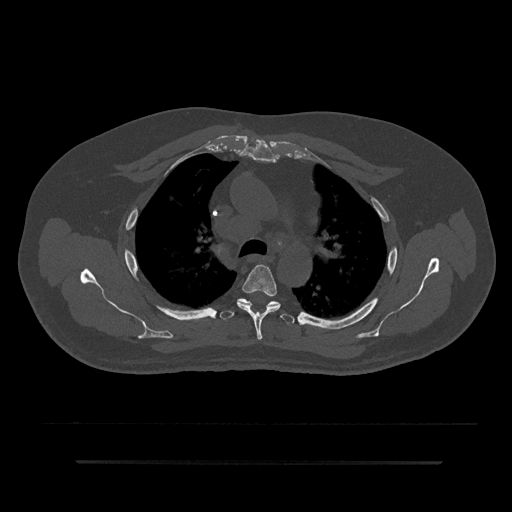
CT including the spine, one axial slice; position 606 of 797 along the scan axis; reconstruction kernel Br40s/3; 120 kVp; bone window (W 1800 / L 400 HU); 0.5 mm slice thickness; 512 × 512 image matrix, field of view 464 × 464 mm. Patient: male, 59 years. From the clinical record (not read from this slice): primary cancer: bile ducts; vertebrae with lytic lesions (as recorded): T10.
Outlined on this slice (semi-automatically segmented with operator editing):
- T4 vertebra: box from (x=237, y=265) to (x=281, y=340) px
- T5 vertebra: (x=220, y=298)–(x=295, y=324)